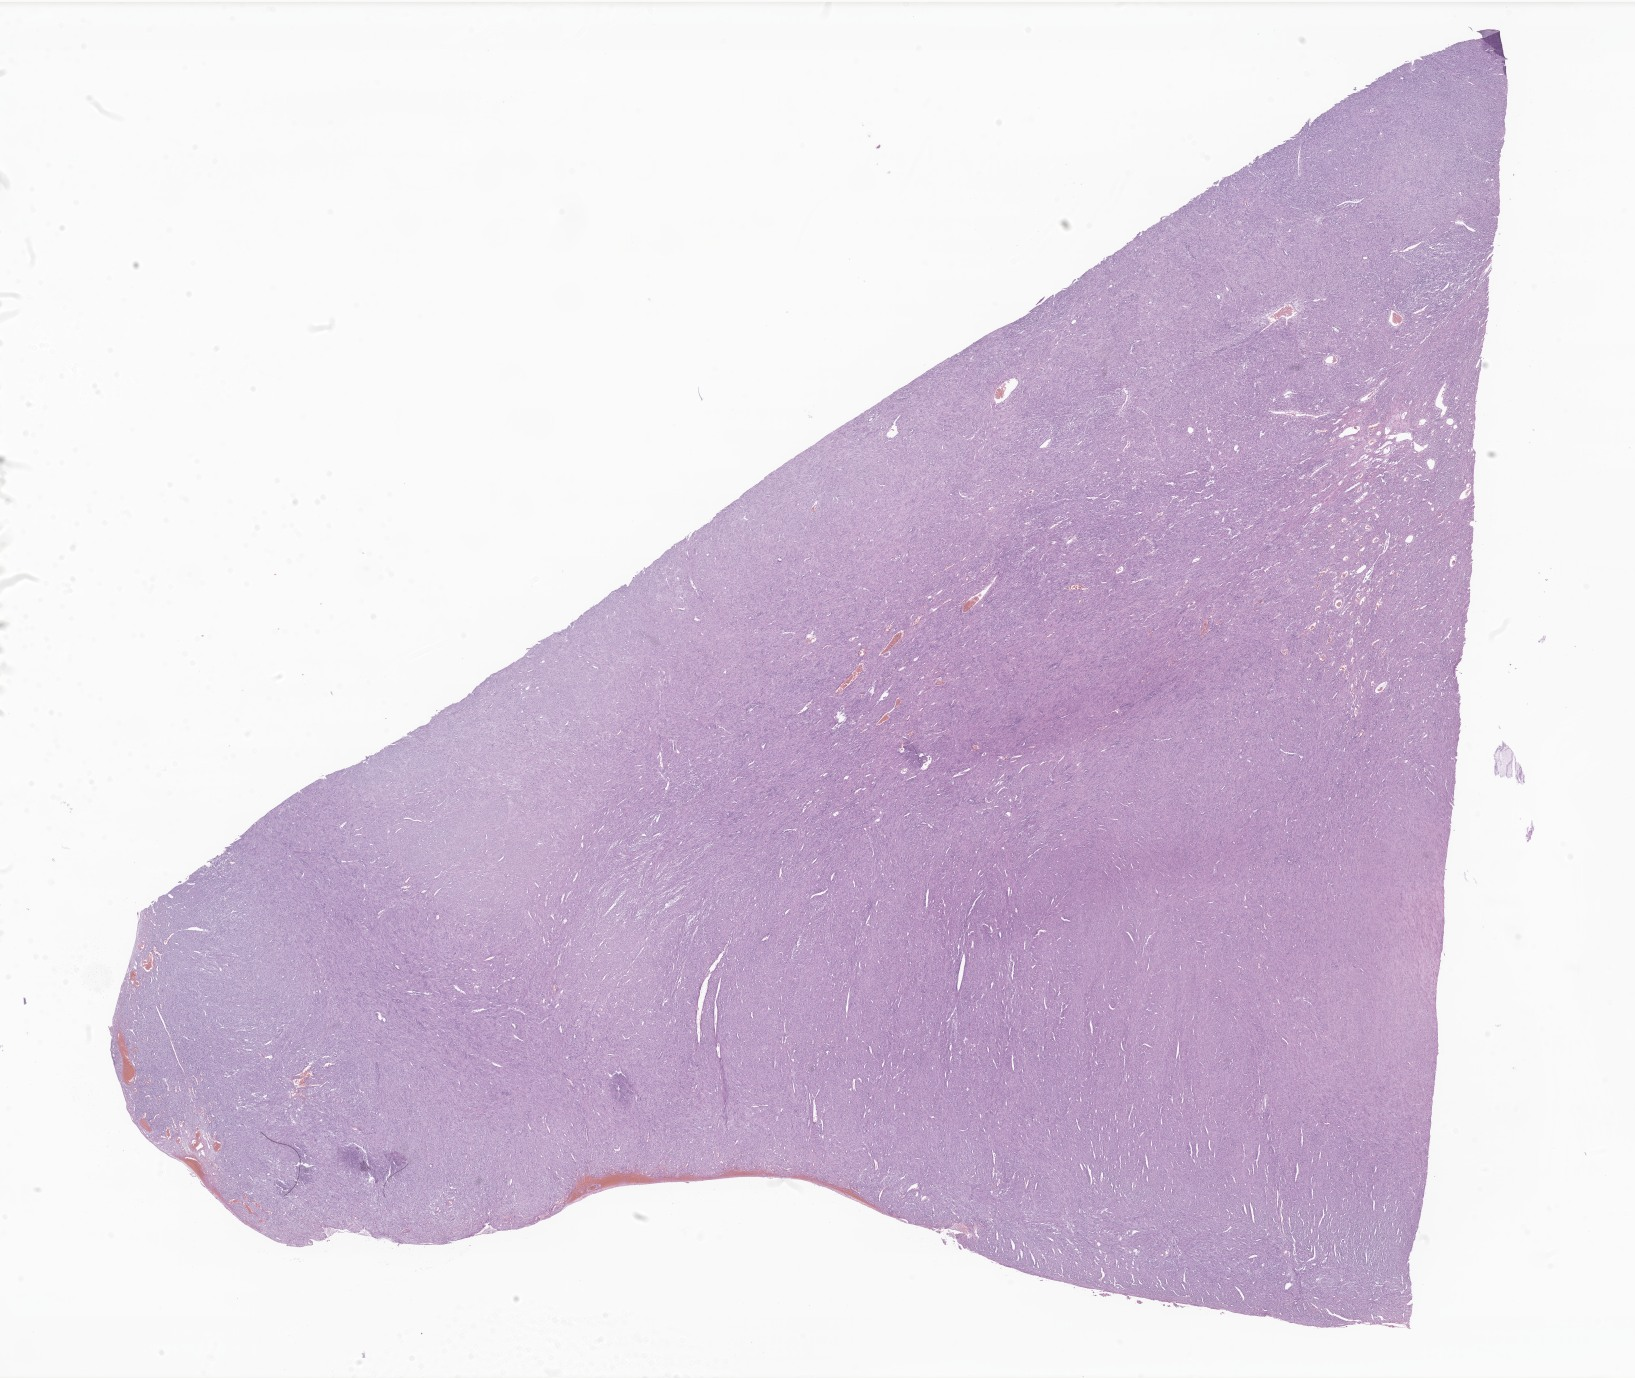
Haematoxylin and eosin whole-slide image of tumor tissue from the abdomen, a low-resolution overview of the entire scanned area, about 27.6 x 23.2 mm; formalin-fixed paraffin-embedded section. Patient female; age 556 days (about 1.5 years).
Diagnosis: Myofibroblastic tumor, NOS.